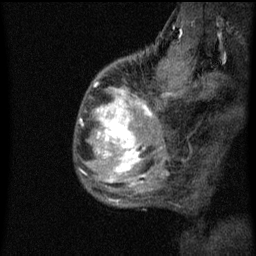
Breast MRI (dynamic contrast-enhanced), one sagittal slice; position 15 of 60 along the scan axis; dynamic contrast-enhanced series, image 2 of 3 at this slice position (ordered by acquisition); 1.5 T; TE 4.2 ms, TR 8 ms; 2 mm slice thickness; 256 × 256 image matrix, field of view 180 × 180 mm. Female patient, age 50 years.
Outlined on this slice (semi-automatically segmented with operator editing):
- analysis volume of interest (the breast-tissue region the enhancement analysis was run in; not a lesion): bounding box (x1, y1, x2, y2) in pixels: (76, 64, 141, 187)
- tumour enhancement mask (voxels above the 70 % enhancement threshold inside the analysis volume of interest): (97, 98, 141, 173)